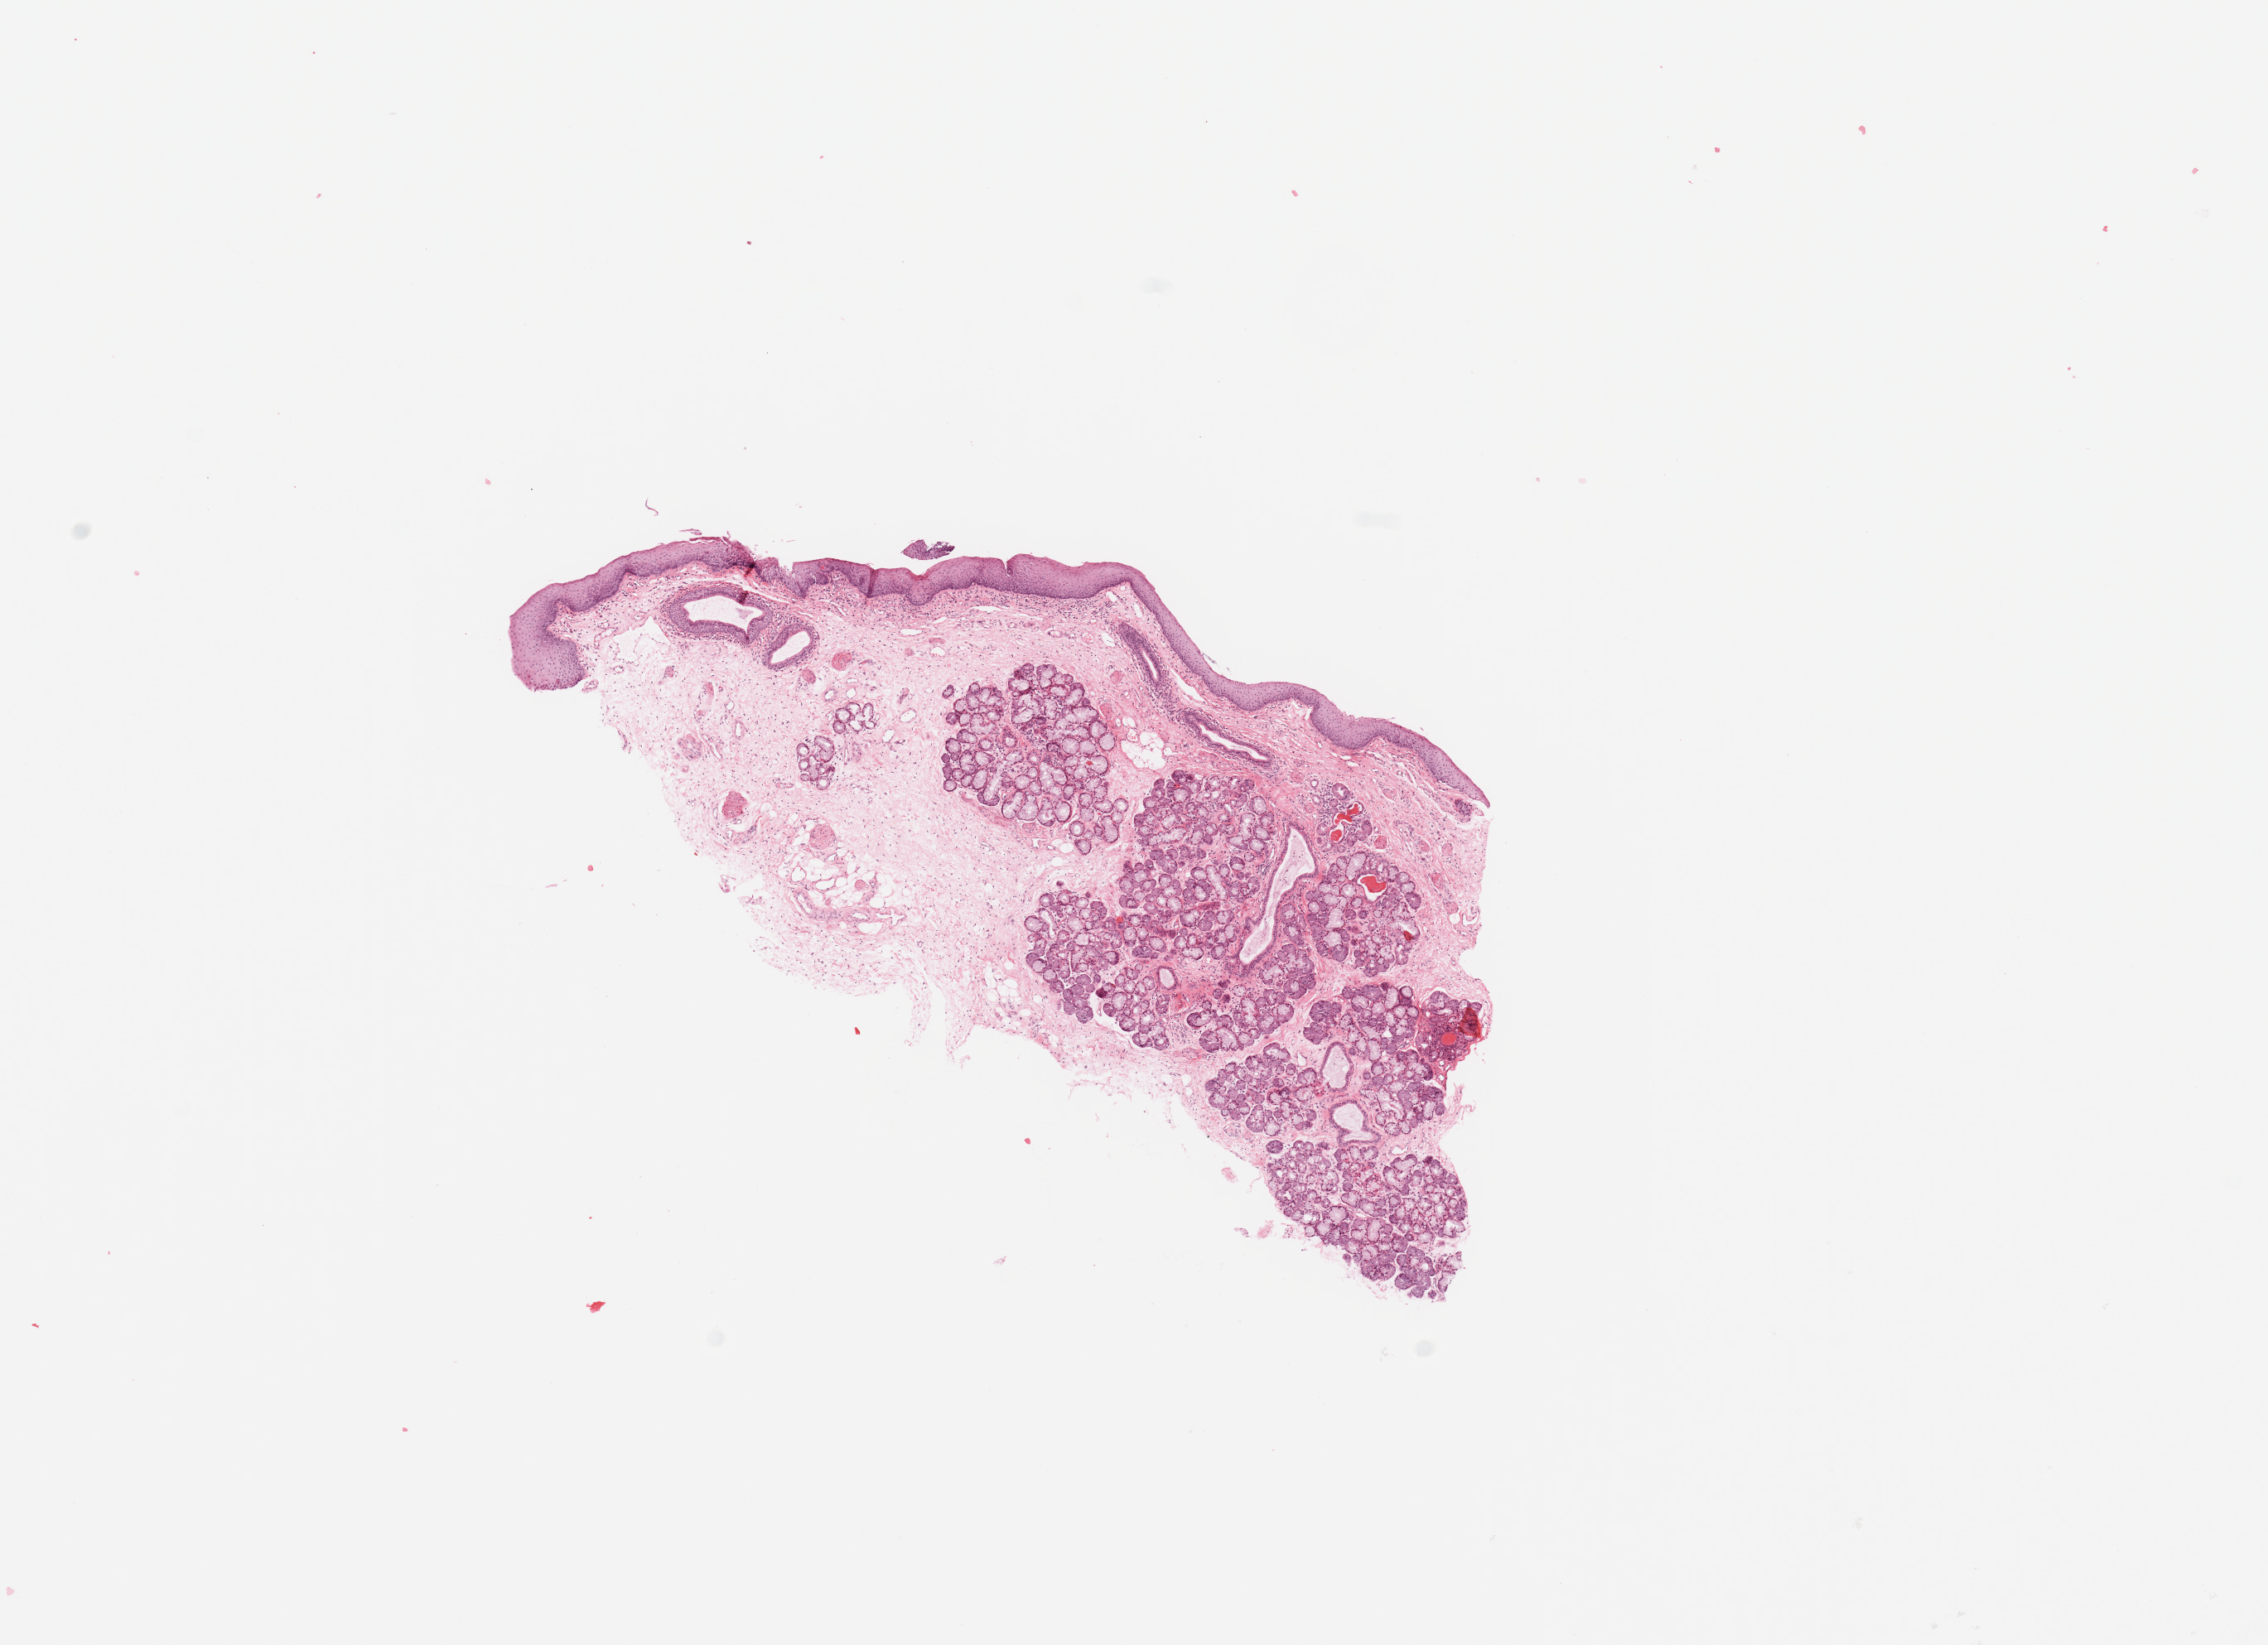
Digitized Hematoxylin and eosin (H&E) stained tissue section (whole slide), whole scanned area (about 10.8 x 7.9 mm) shown as a low-resolution overview, normal (non-tumour) tissue sample, sampled site: larynx. 63-year-old female patient.
This section: normal (non-tumour) tissue from the same patient. Patient diagnosis: Squamous cell carcinoma, NOS (larynx, NOS).